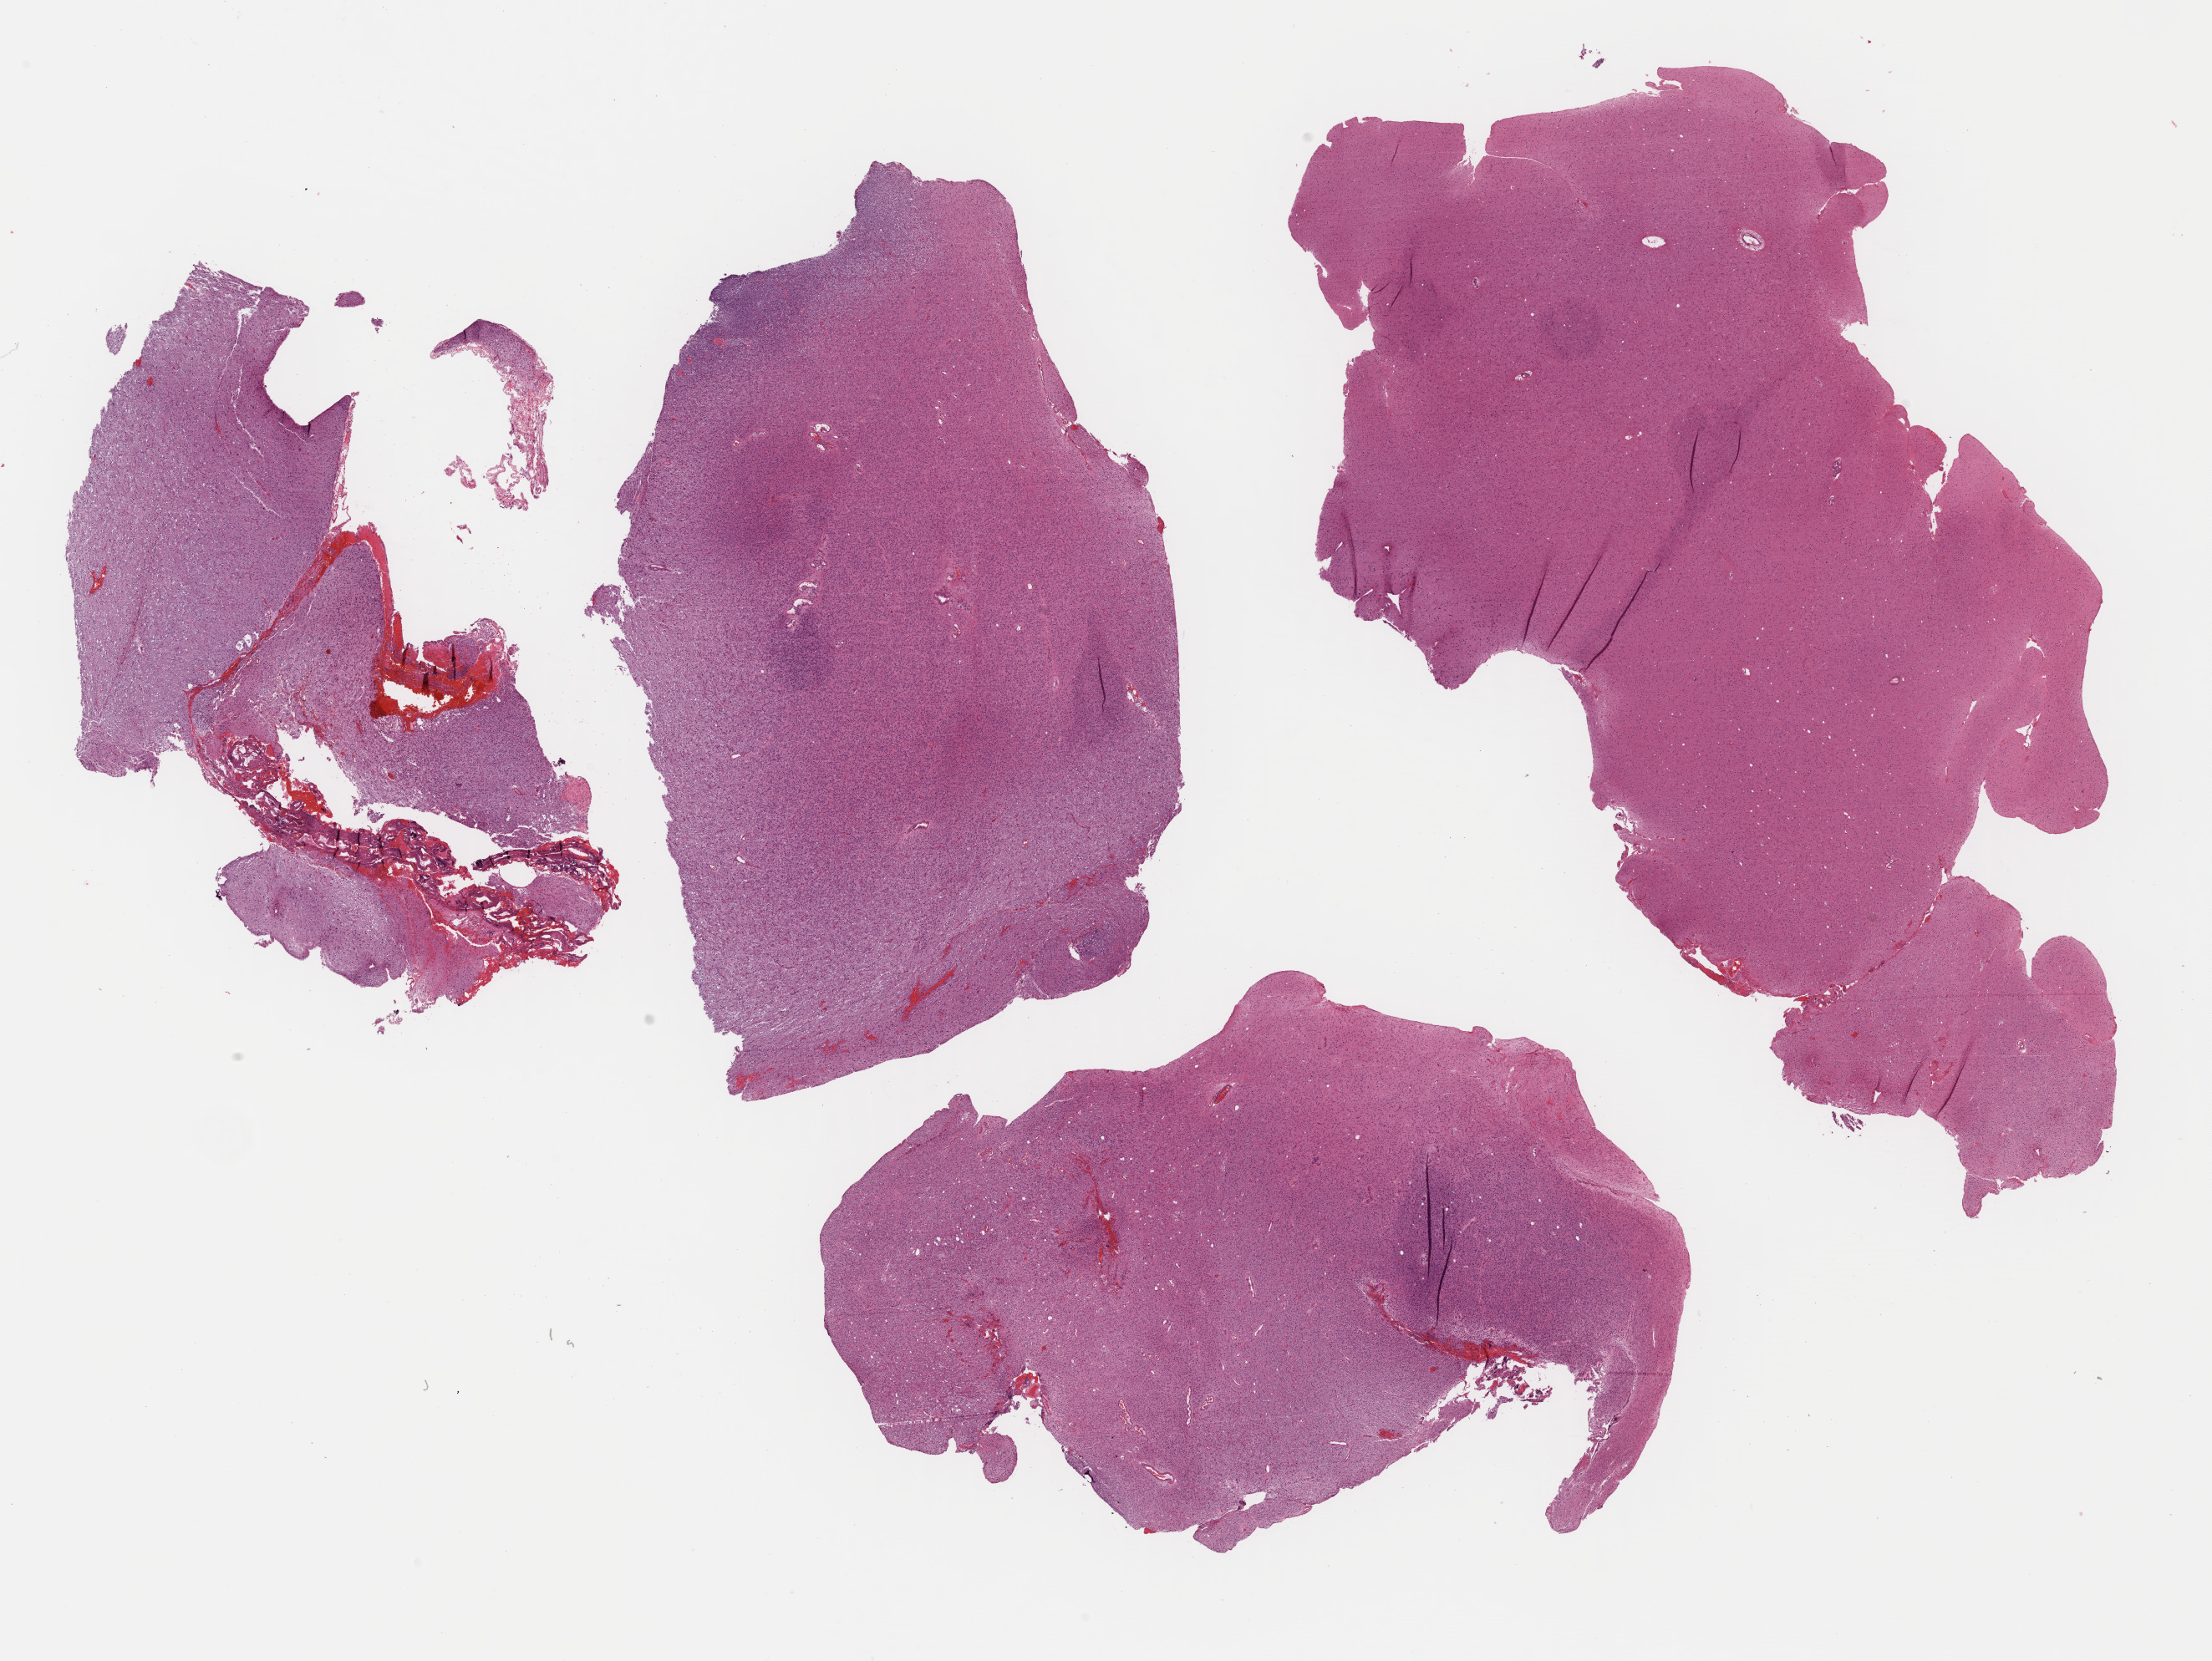
Digitized H&E tissue section (whole slide), a low-resolution overview of the entire scanned area, about 20.8 x 15.6 mm. Formalin-fixed paraffin-embedded (FFPE) diagnostic section. Primary tumour sample from the brain. Patient: male, age at initial diagnosis 30 years.
Histologic diagnosis: Oligodendroglioma, anaplastic (cerebrum).